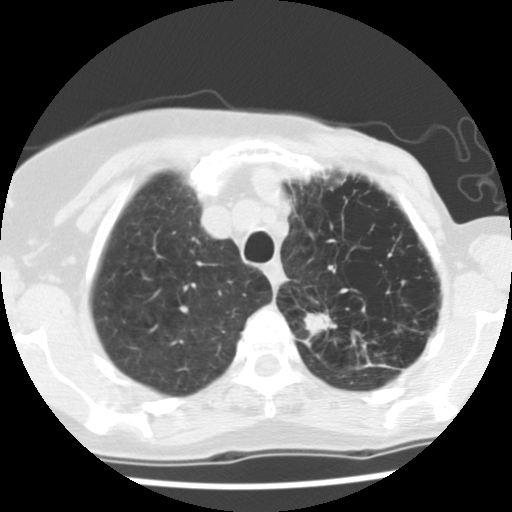
Low-dose screening chest CT, axial slice. Baseline screening round. Lung window (W 1500 / L -600 HU). 2.5 mm slice thickness. 140 kVp. Slice 25 of 128 in the series. 512 × 512 image matrix, field of view 290 × 290 mm. Female participant, aged 67 years at enrolment. Current smoker at enrolment.
Expert-annotated lung lesion, bounding box [x1, y1, x2, y2] px = [291, 296, 387, 378]. The screening reader recorded 2 non-calcified nodules or masses ≥4 mm on this exam (left upper lobe, left lower lobe); which of them this box marks is not recorded. Official screen result: positive, change unspecified: nodule(s) >= 4 mm or enlarging nodule(s), mass(es), or other non-specific abnormalities suspicious for lung cancer. Participant outcome: lung cancer diagnosed 109 days after this screen — adenocarcinoma, NOS, left upper lobe, poorly differentiated (G3), stage IIB (AJCC 6th edition), 45 mm at pathology.